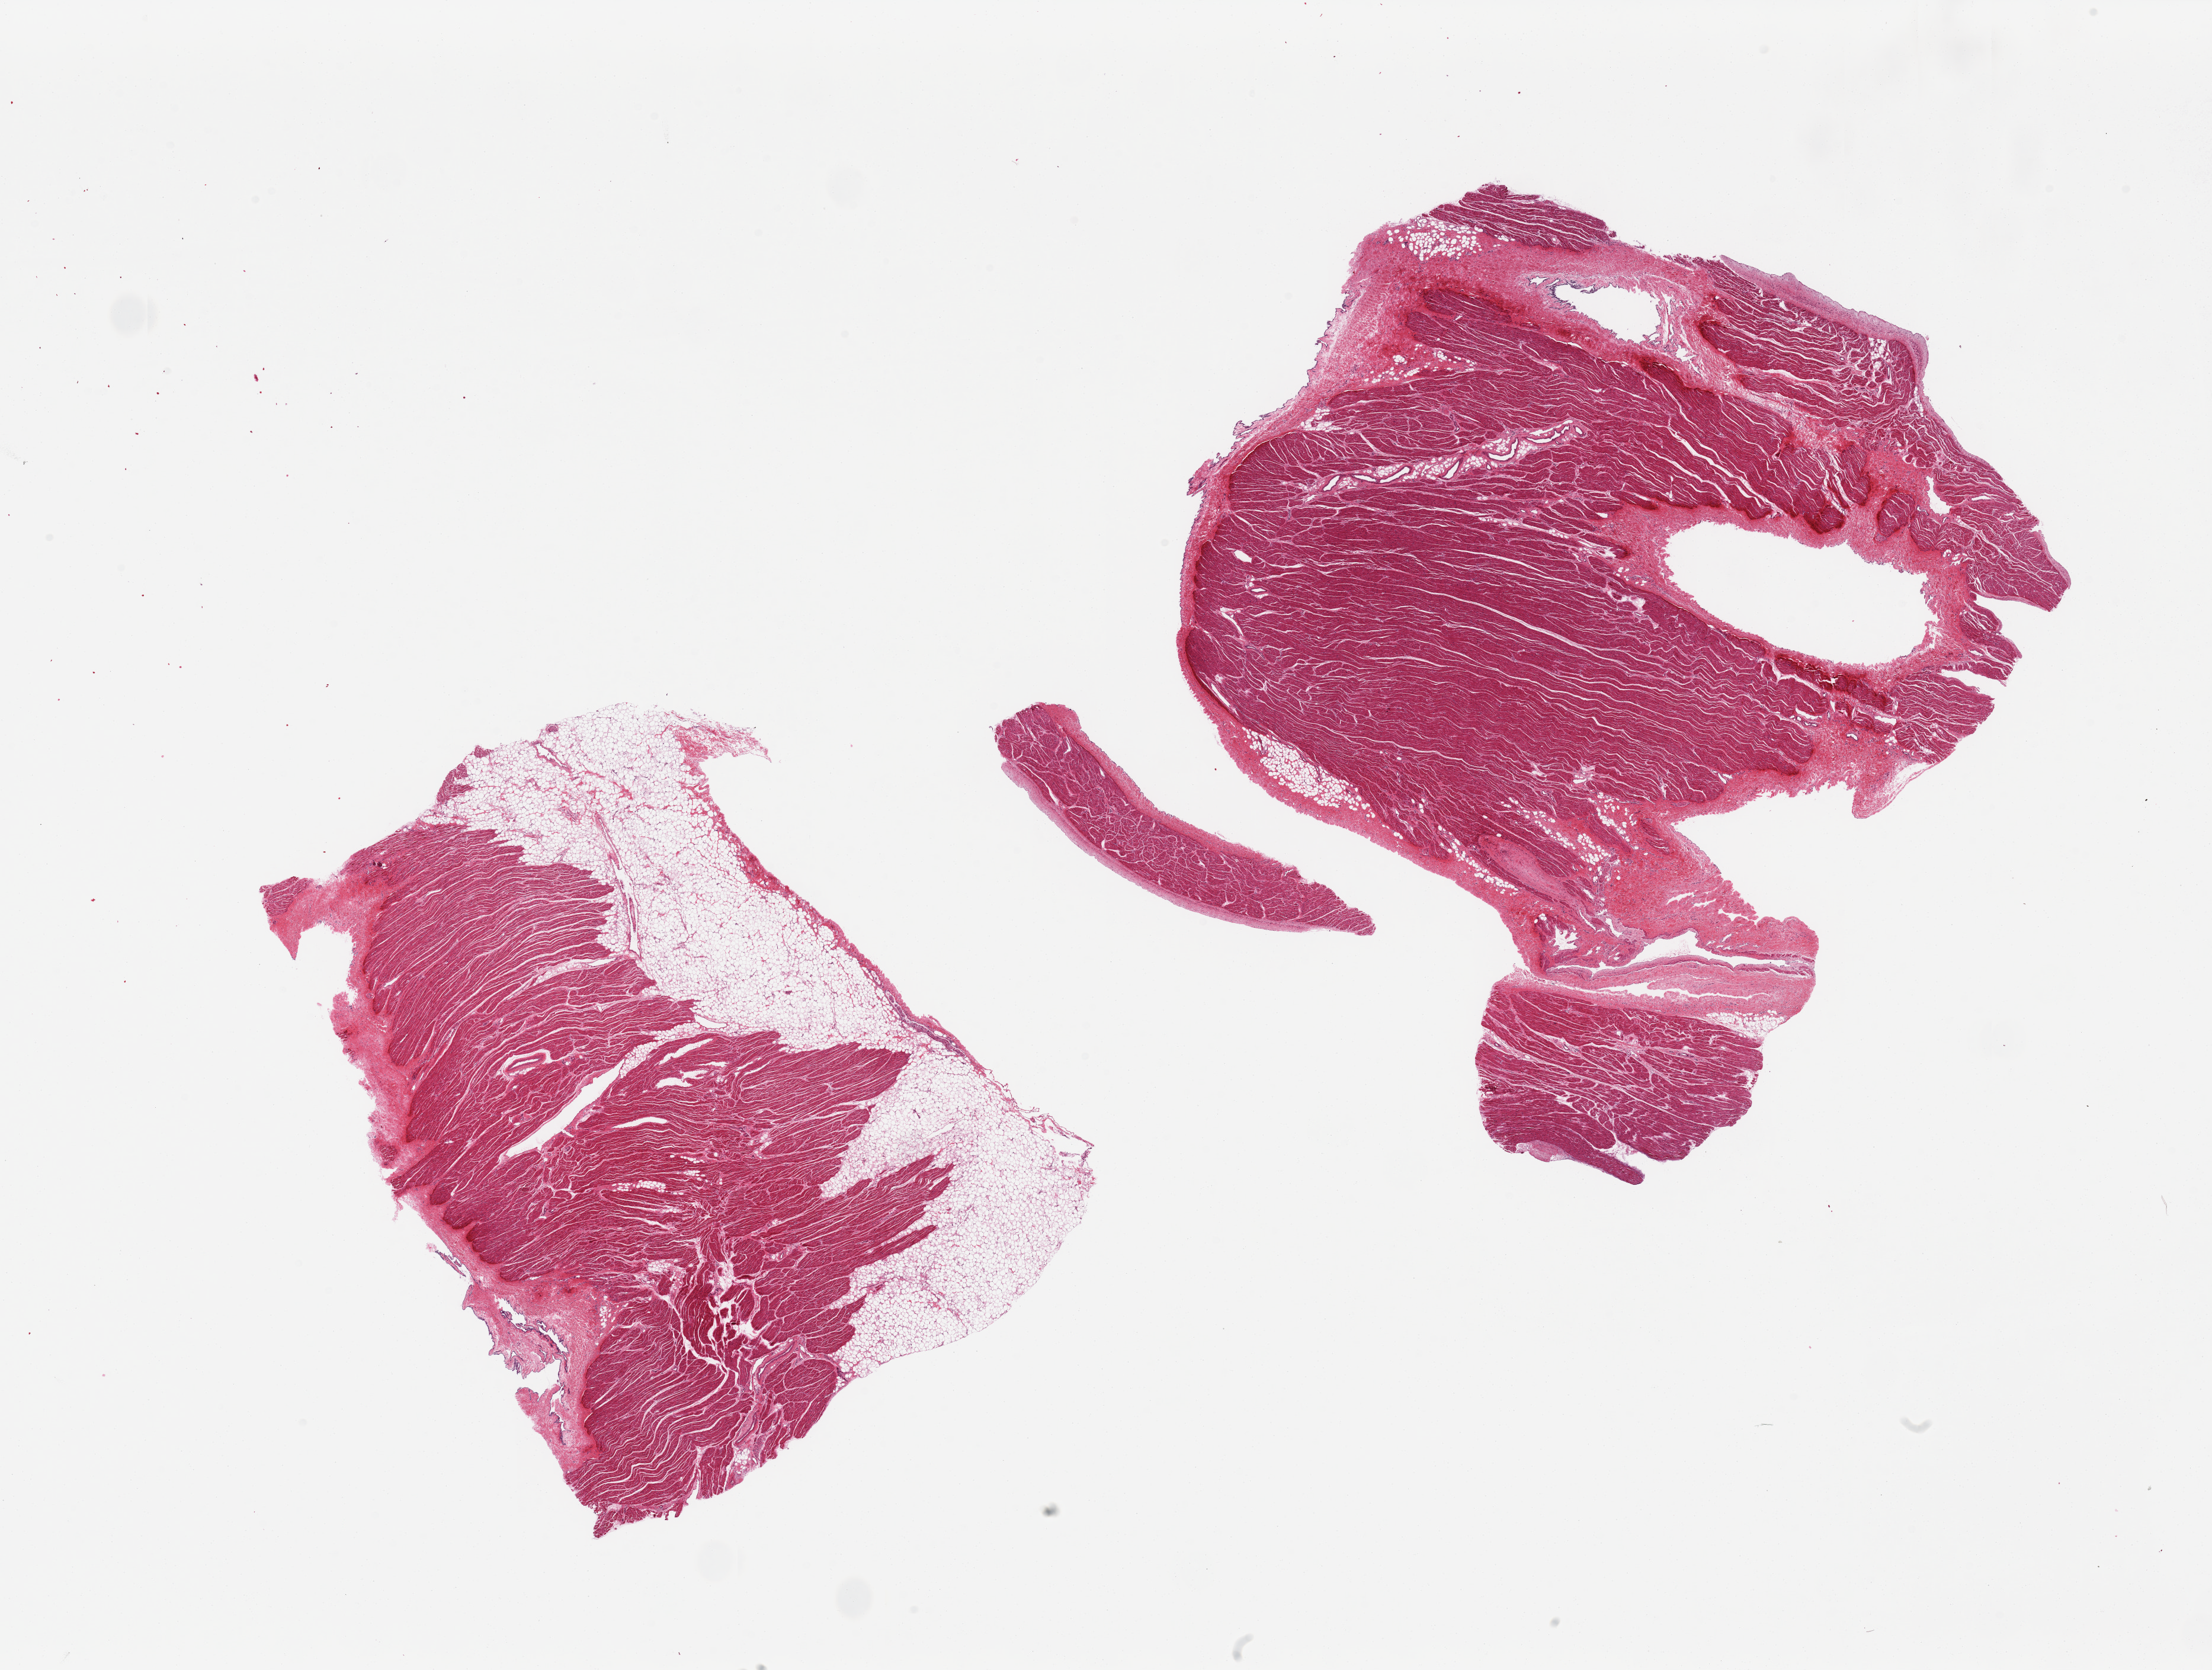
Whole-slide image, hematoxylin and eosin (H&E) stain, brightfield, low-resolution overview of the scanned area, about 29.5 x 22.3 mm; PAXgene-fixed, paraffin-embedded tissue; sampled site (target tissue): auricular appendage; donor tissue sample. Male donor.
- reviewer comment on this tissue sample: 2 pieces, one piece is 40% fat